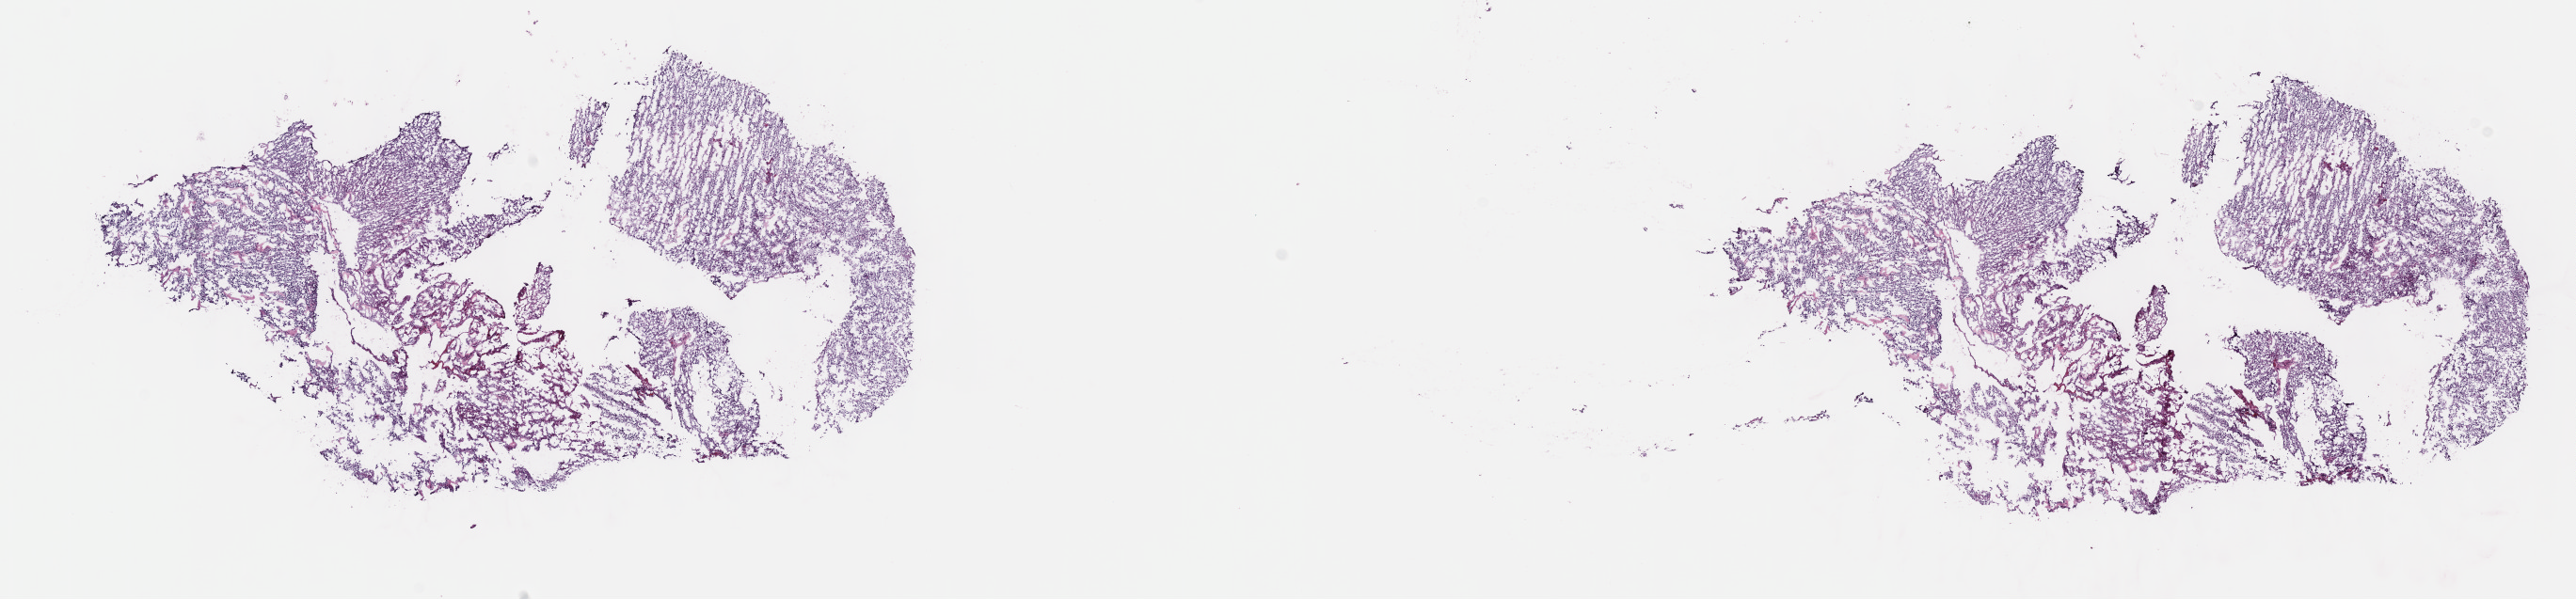
Whole-slide histology image, Hematoxylin and eosin (H&E) stained, shown as a low-resolution overview of the whole scanned area (about 22.1 x 5.2 mm), frozen section from the top of the tissue portion, brain, primary tumour sample. Female patient; age at initial diagnosis 35 years. Histologic grade: G3 (poorly differentiated). Pathologist review of this section (percent, as recorded): tumour cells 70%, tumour nuclei 90%, normal cells 10%, stromal cells 20%, necrosis 0%. Infiltration values recorded for this section: lymphocyte infiltration 0%, monocyte infiltration 0%, neutrophil infiltration 0%.
• pathologic diagnosis: Oligodendroglioma, anaplastic (cerebrum)